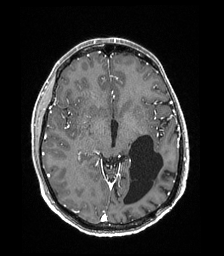
Brain MRI from a brain-tumour surgery series, one axial slice; position 101 of 192 along the scan axis; T1-weighted post-contrast; 1 mm slice thickness; 224 × 256 image matrix. From the clinical record (not read from this slice): histopathology: Low grade glioma; IDH mutation: no; tumour location: Left Parieto-Occipital Intraventricular.
Outlined on this slice (expert manual segmentation):
- previous resection cavity: box from (x=124, y=135) to (x=163, y=205) px